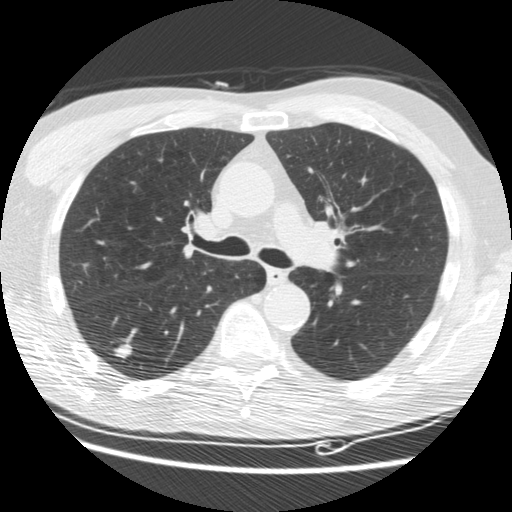
Low-dose screening chest CT, one axial slice; slice 109 of 176 in the series (ordered by position); lung window (W 1500 / L -600 HU); 2.5 mm slice thickness; 512 × 512 image matrix, field of view 347 × 347 mm.
Annotated regions visible in this slice (manually delineated by an expert):
- lesion 1 (tumor, lower lobe of right lung): box from (x=114, y=344) to (x=132, y=358) px